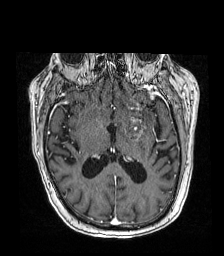
Brain MRI from a brain-tumour surgery series, one axial slice. Position 87 of 192 along the scan axis. T1-weighted post-contrast. 1 mm slice thickness. 224 × 256 image matrix. Case-level facts recorded for this patient, not image findings: histopathology: Metastatic carcinoma from lung primary; tumour location: Left Frontal Caudate.
Annotated regions visible in this slice (expert manual segmentation):
- tumour: bounding box [x1, y1, x2, y2] px = [117, 115, 148, 139]